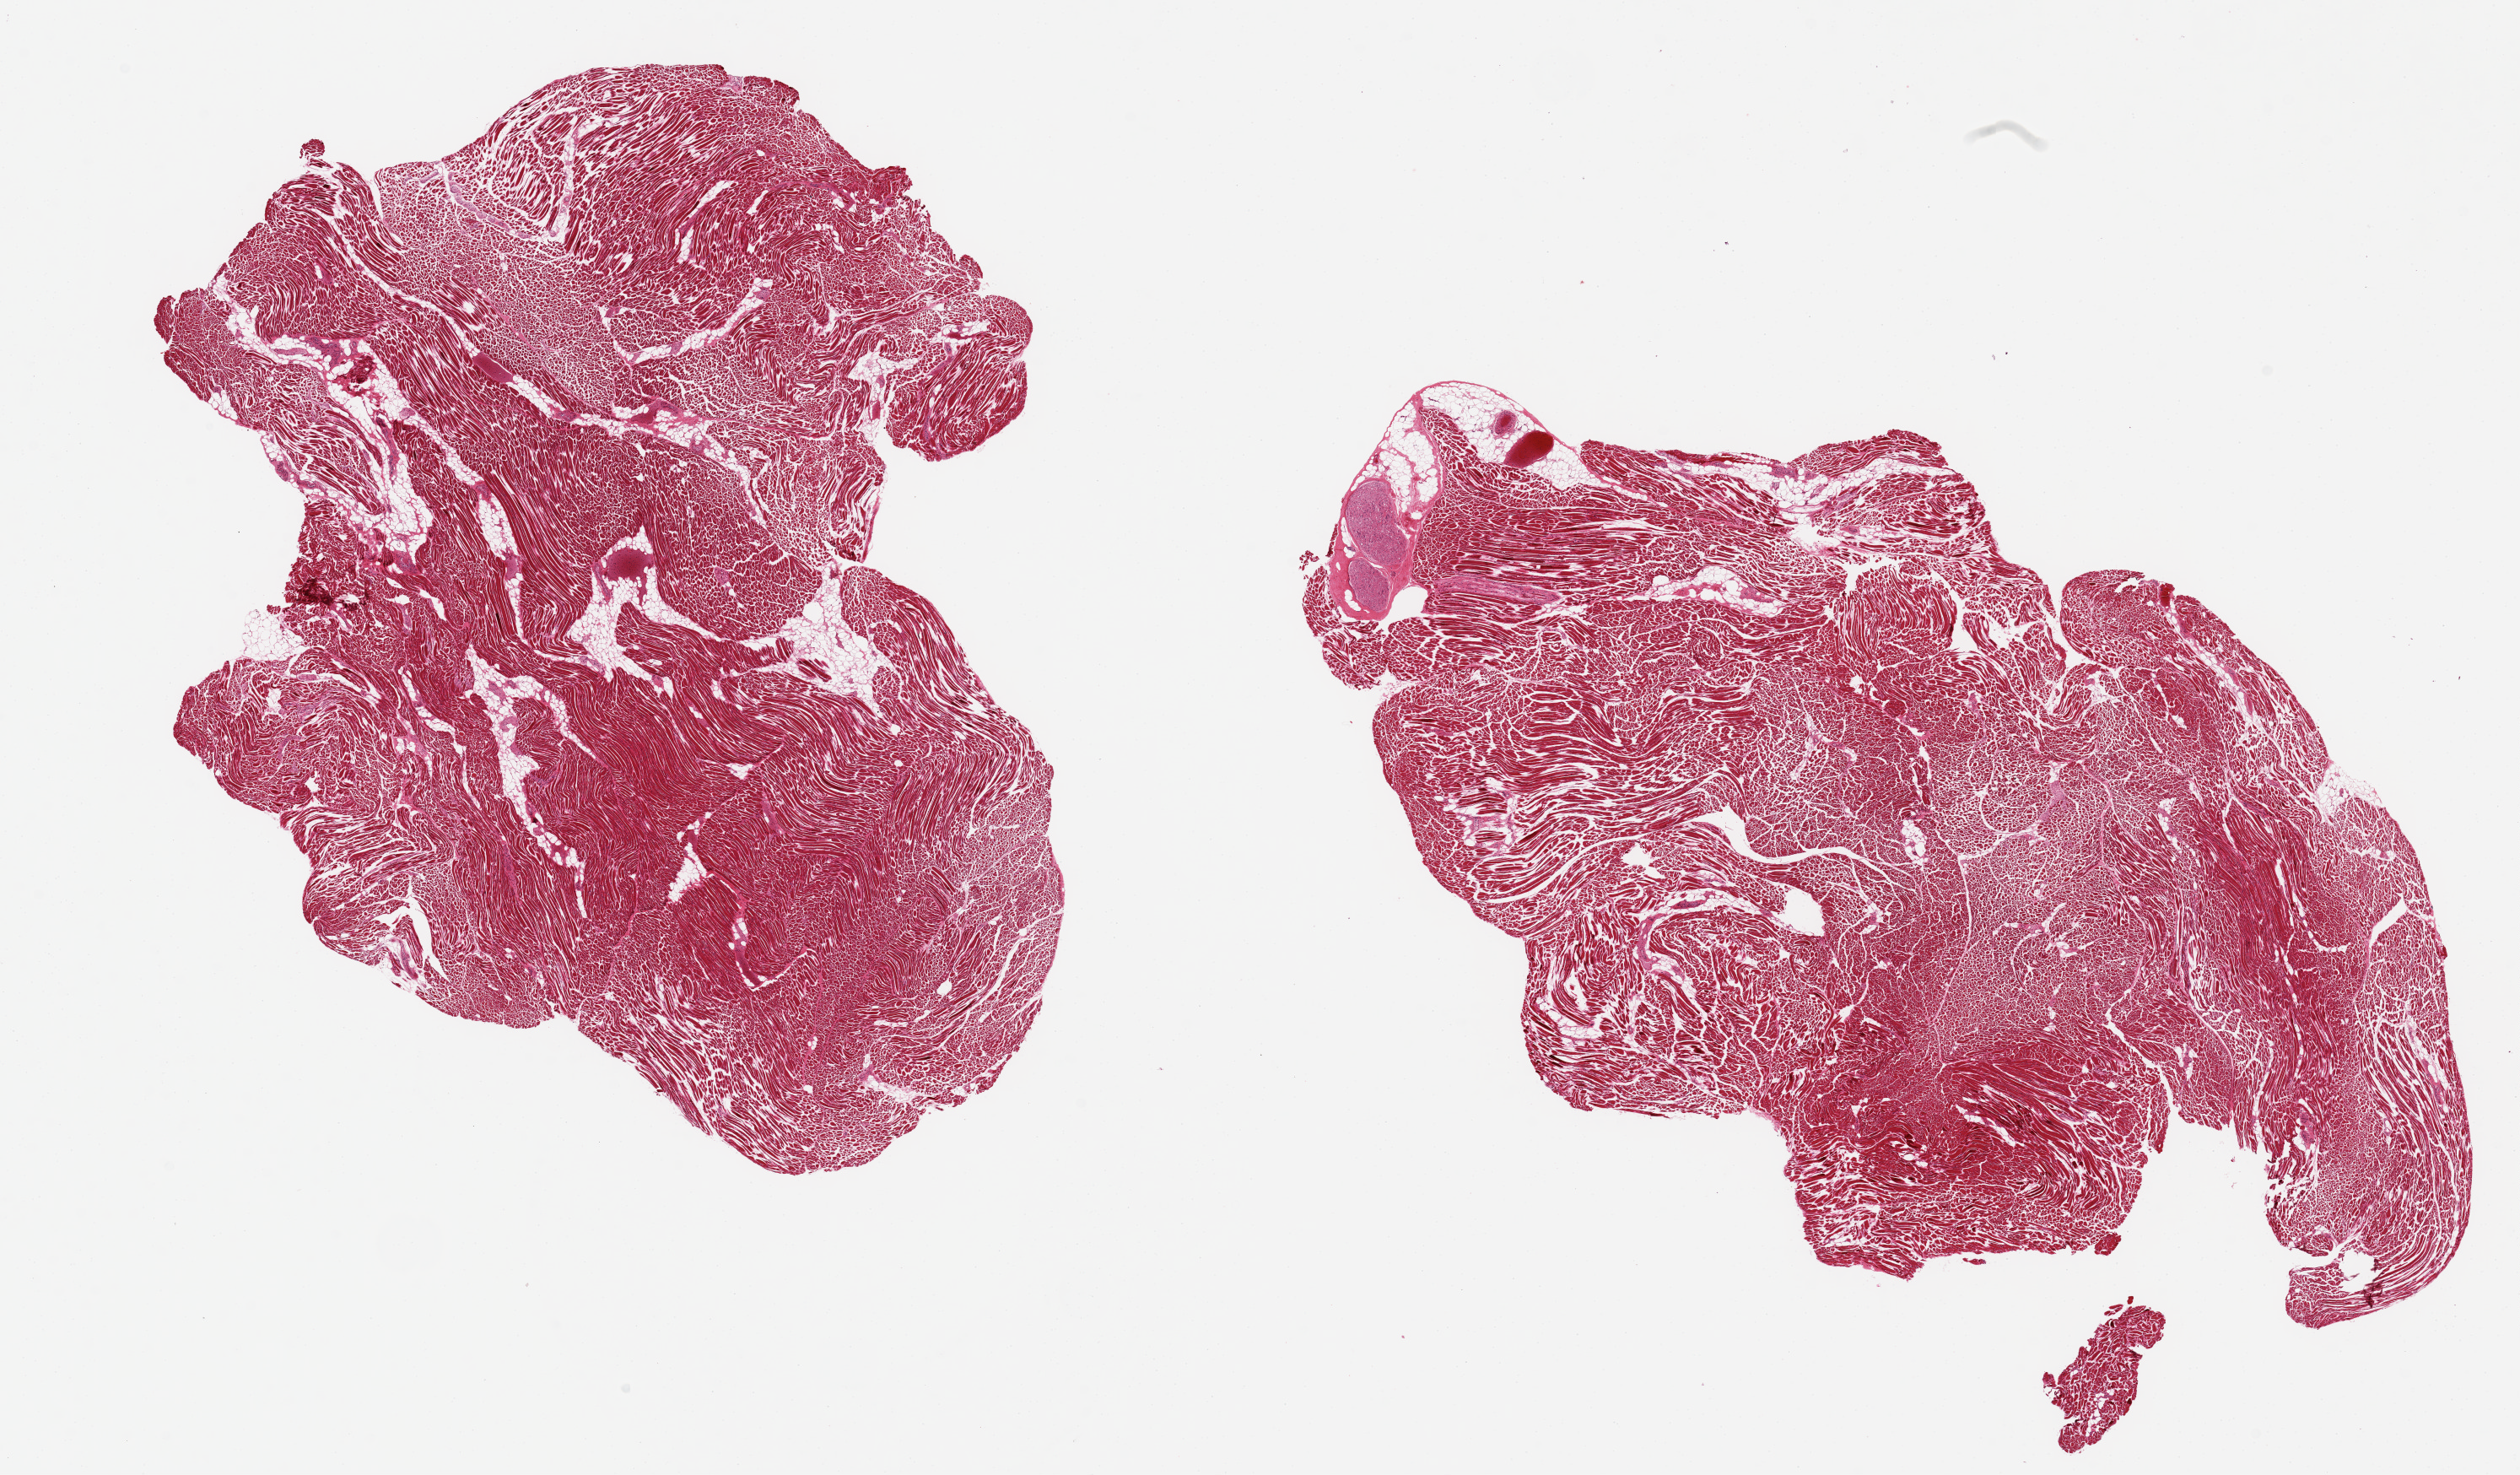
Whole-slide image, haematoxylin and eosin stain — a low-resolution overview of the entire scanned area, about 23.6 x 13.8 mm; PAXgene-fixed, paraffin-embedded tissue; target tissue: skeletal muscle; tissue donor sample. Donor: female.
Review note (as recorded): 2 aliquots, ~8x7mm. One has 1.2x0.5mm peripheral nerve on one edge.